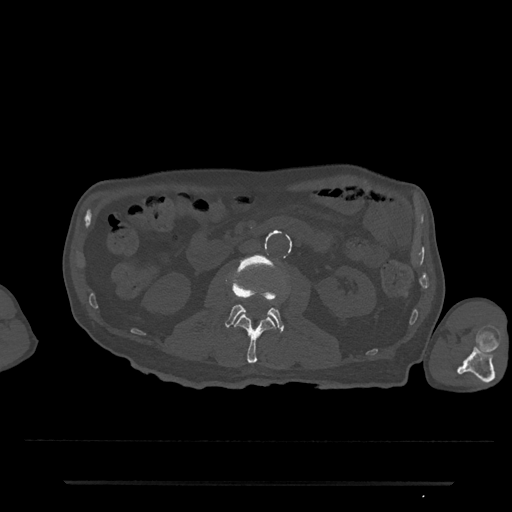
CT including the spine, one axial slice. Slice 25 of 797 in the series (ordered by position). Reconstruction kernel Br40s/3. Bone window (W 1800 / L 400 HU). 0.5 mm slice thickness. 512 × 512 image matrix. Male patient, age 74 years. Case-level facts recorded for this patient, not image findings: primary cancer: prostate.
Structures marked on this image (semi-automatic segmentation, software-assisted and operator-edited):
- L2 vertebra: box from (x=236, y=315) to (x=276, y=364) px
- L3 vertebra: (x=225, y=255)–(x=284, y=333)